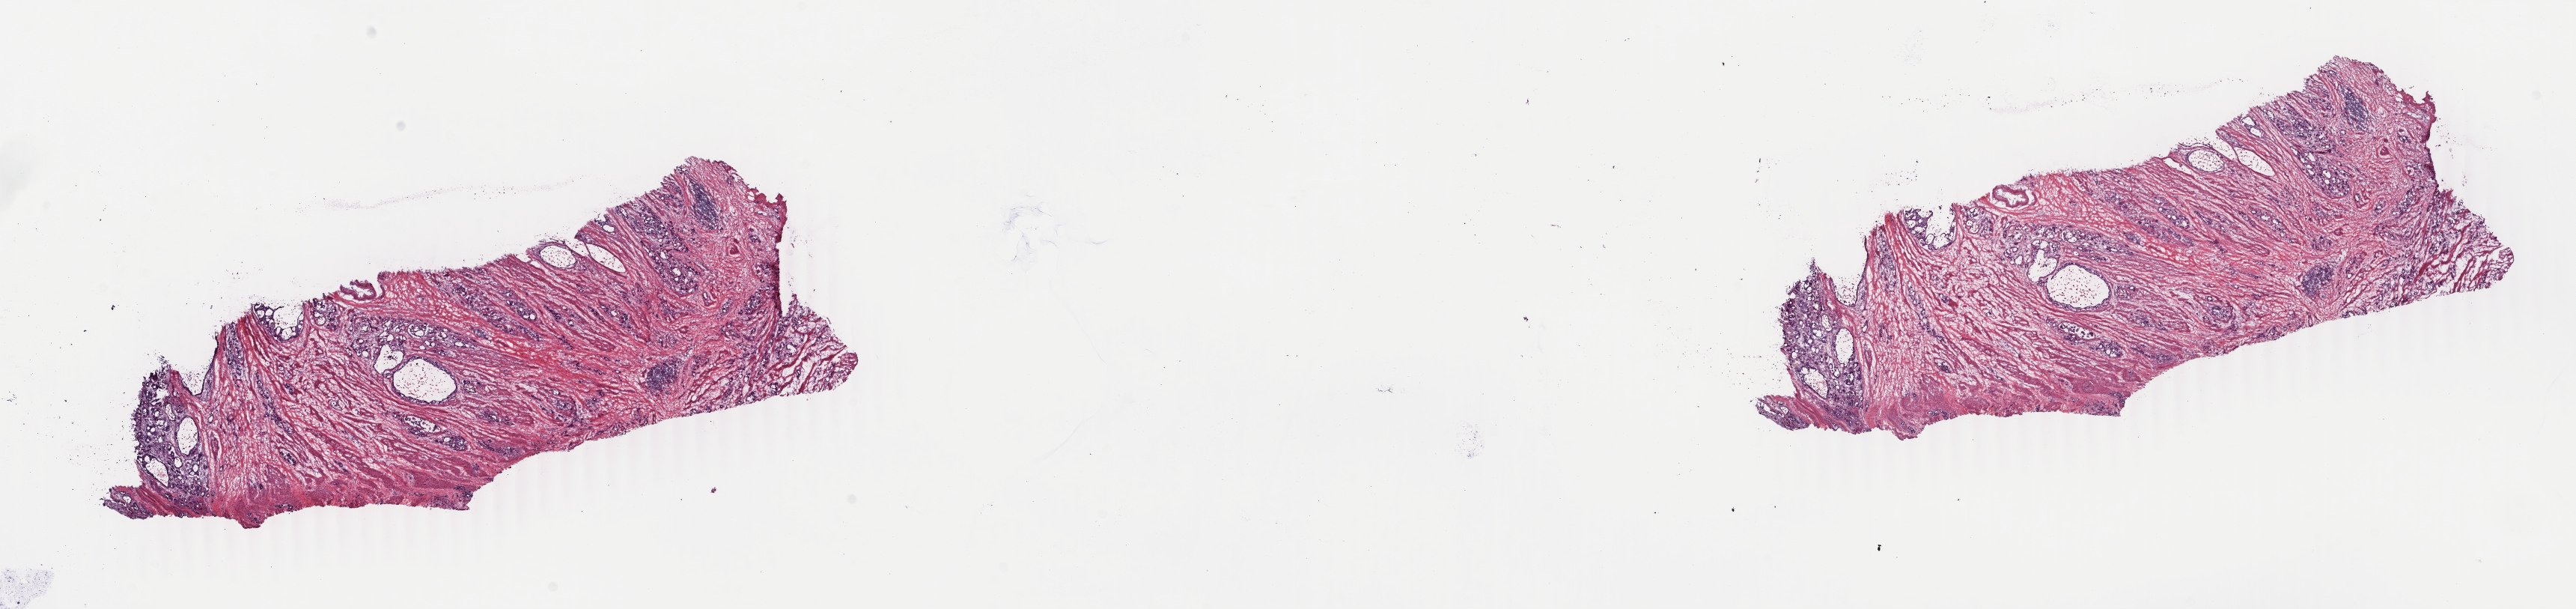
Digitized H&E-stained tissue section (whole slide) — low-resolution overview of the scanned area, about 27.4 x 6.5 mm. Frozen section from the top of the tissue portion. Stomach, primary tumour sample. Female, age 71 years at initial diagnosis. Histologic grade: G3 (poorly differentiated). Slide review estimates, as recorded: tumour cells 26%, tumour nuclei 70%, normal cells 0%, stromal cells 70%, necrosis 4%. Infiltration values recorded for this section: lymphocyte infiltration 4%, monocyte infiltration 0%, neutrophil infiltration 0%.
• lymph nodes positive (case pathology): 12 of 12 examined
• AJCC pathologic stage: IIIB (7th edition)
• diagnosis: Adenocarcinoma, NOS (cardia, NOS)